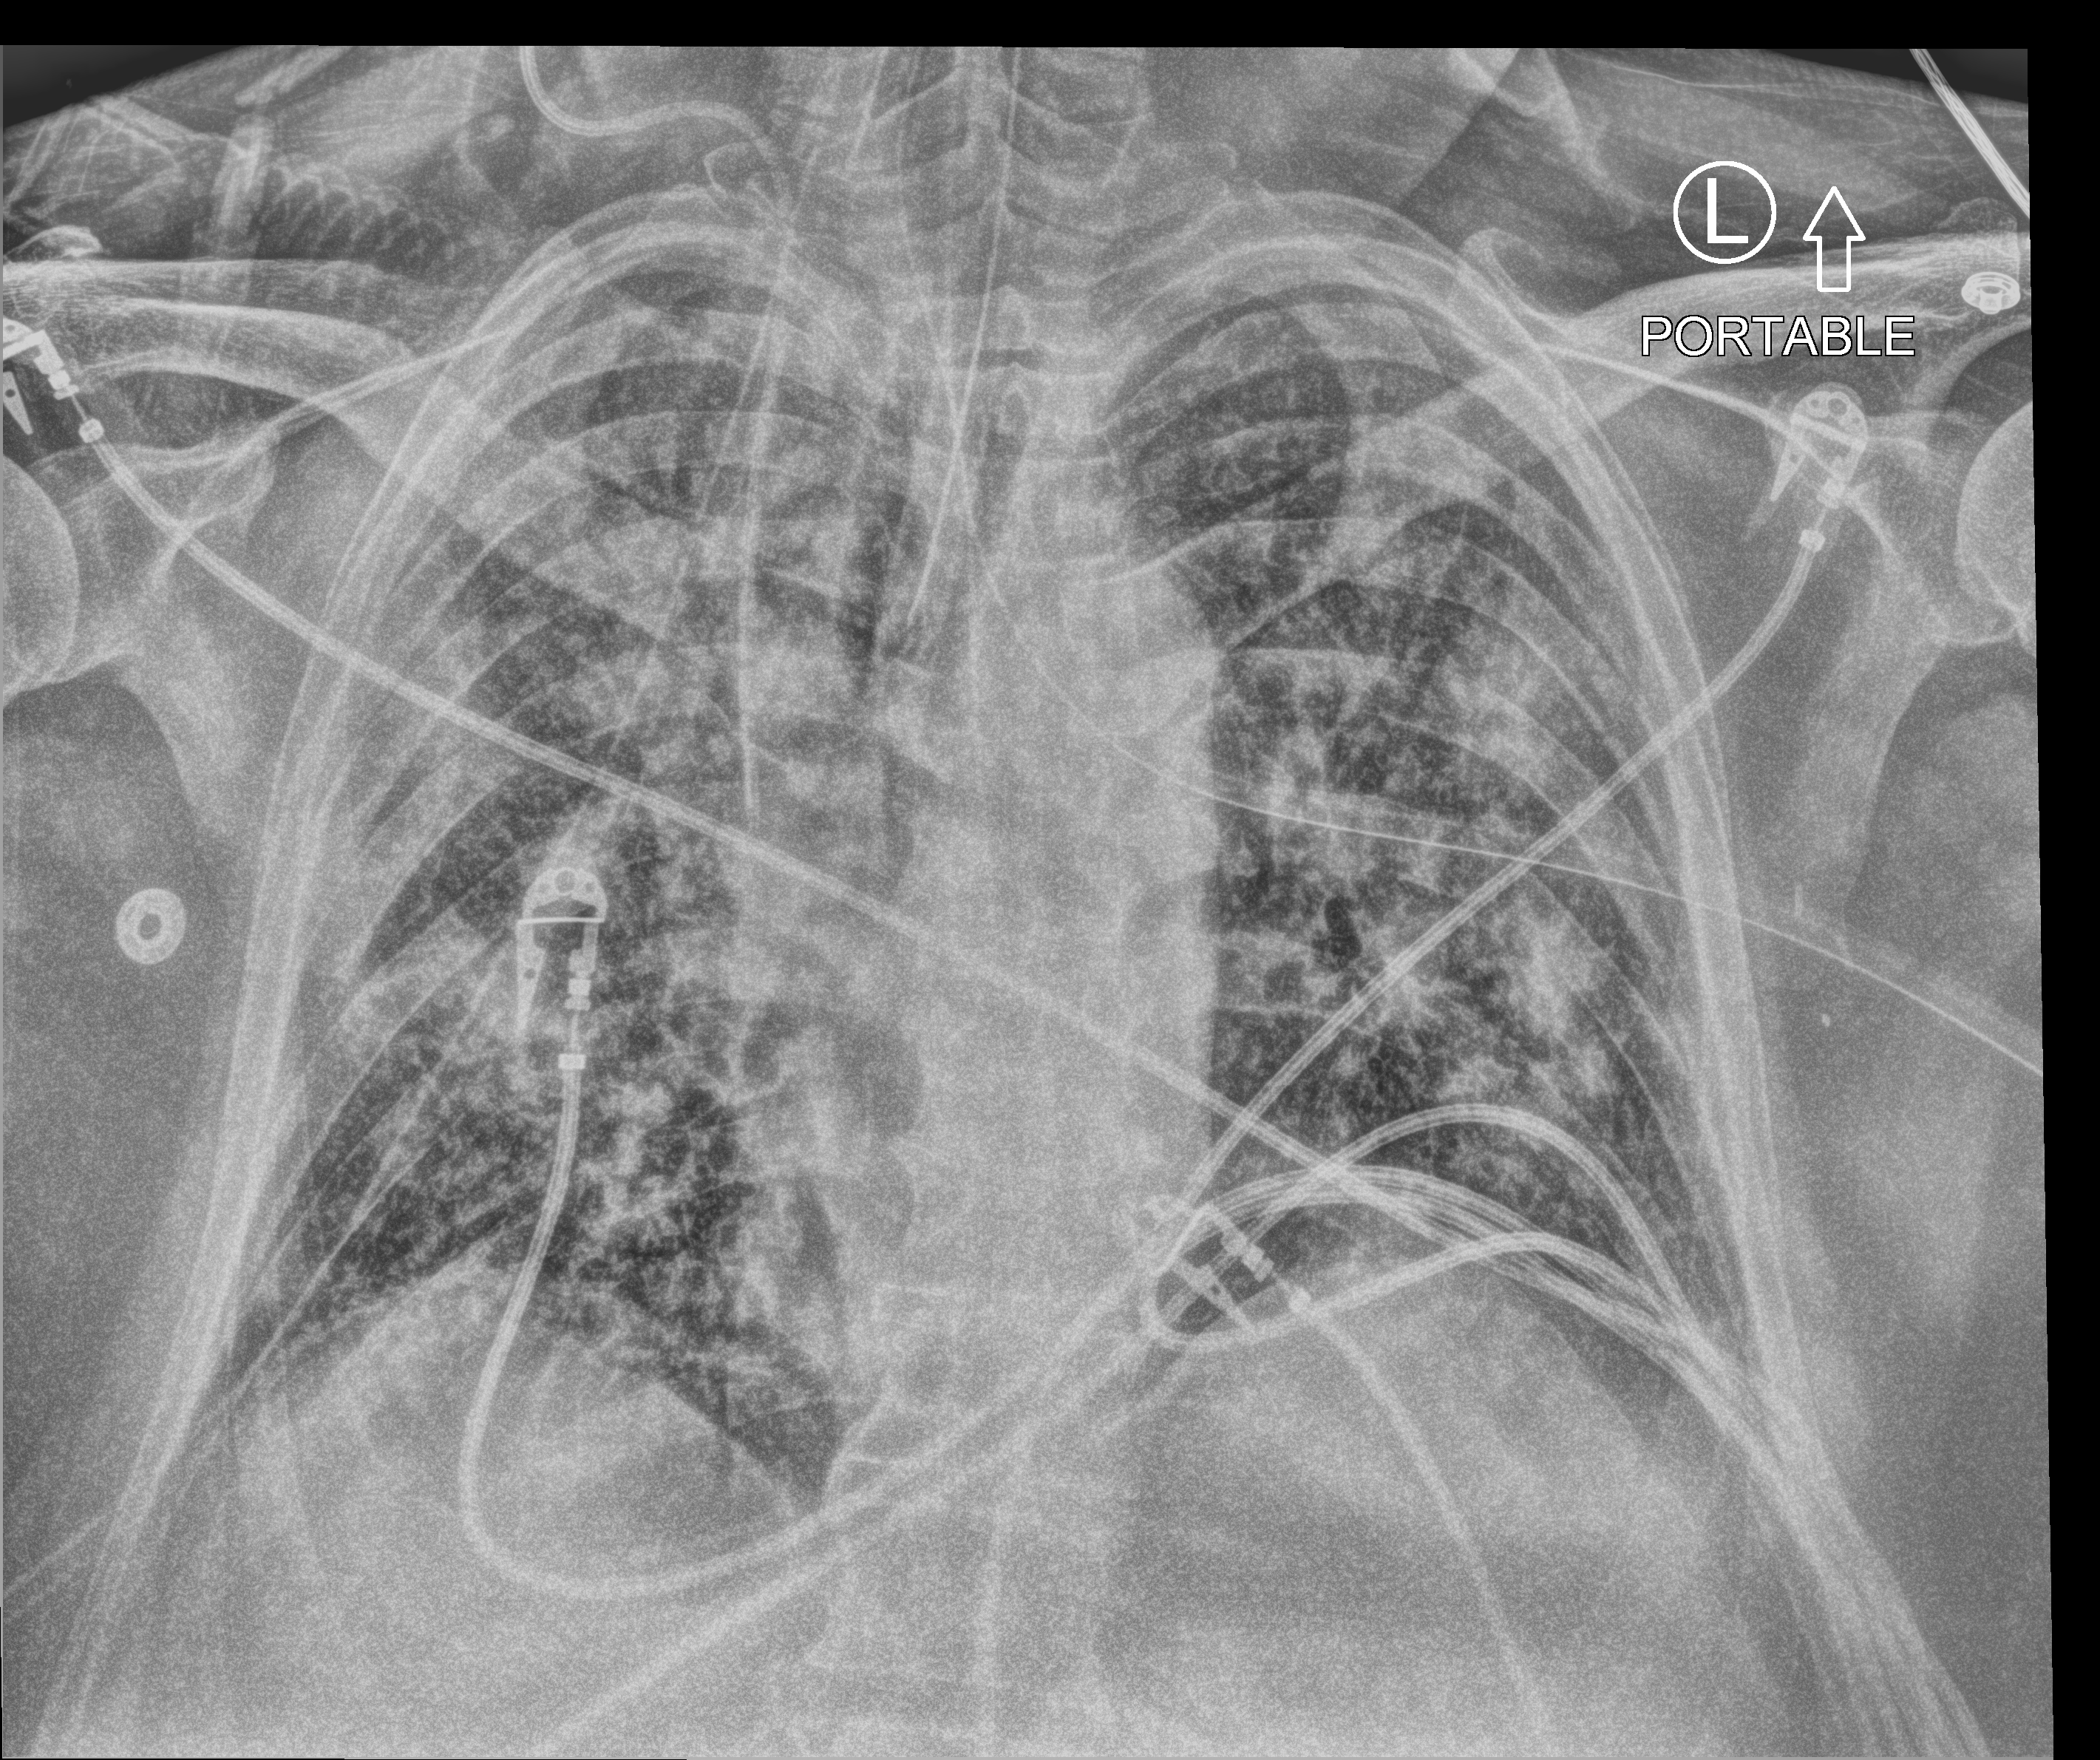
Chest X-ray (portable), anteroposterior (AP) projection. Male patient hospitalised with COVID-19, age 60–74 years.
Hospital-stay facts (about this admission, not read from this image; timing relative to this image not recorded): length of hospital stay: 17 days; mechanically ventilated during this hospital stay: yes.